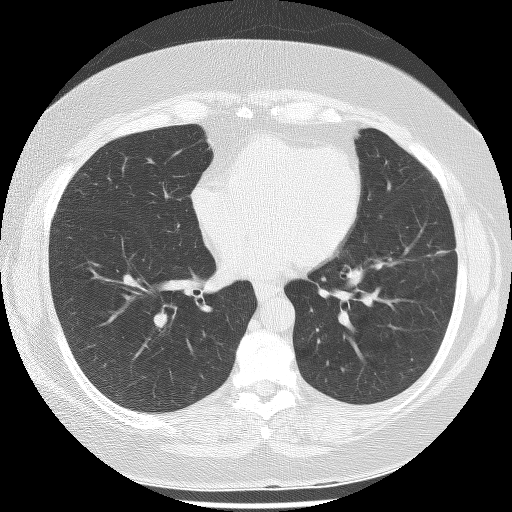
Low-dose screening chest CT, one axial slice; position 110 of 233 along the scan axis; reconstruction kernel BONE; lung window (W 1500 / L -600 HU); 2.5 mm slice thickness; 512 × 512 image matrix, field of view 340 × 340 mm.
Annotated regions visible in this slice (outlined manually by an expert reader):
- lesion 1 (tumor, lower lobe of left lung): box from (x=427, y=251) to (x=450, y=256) px